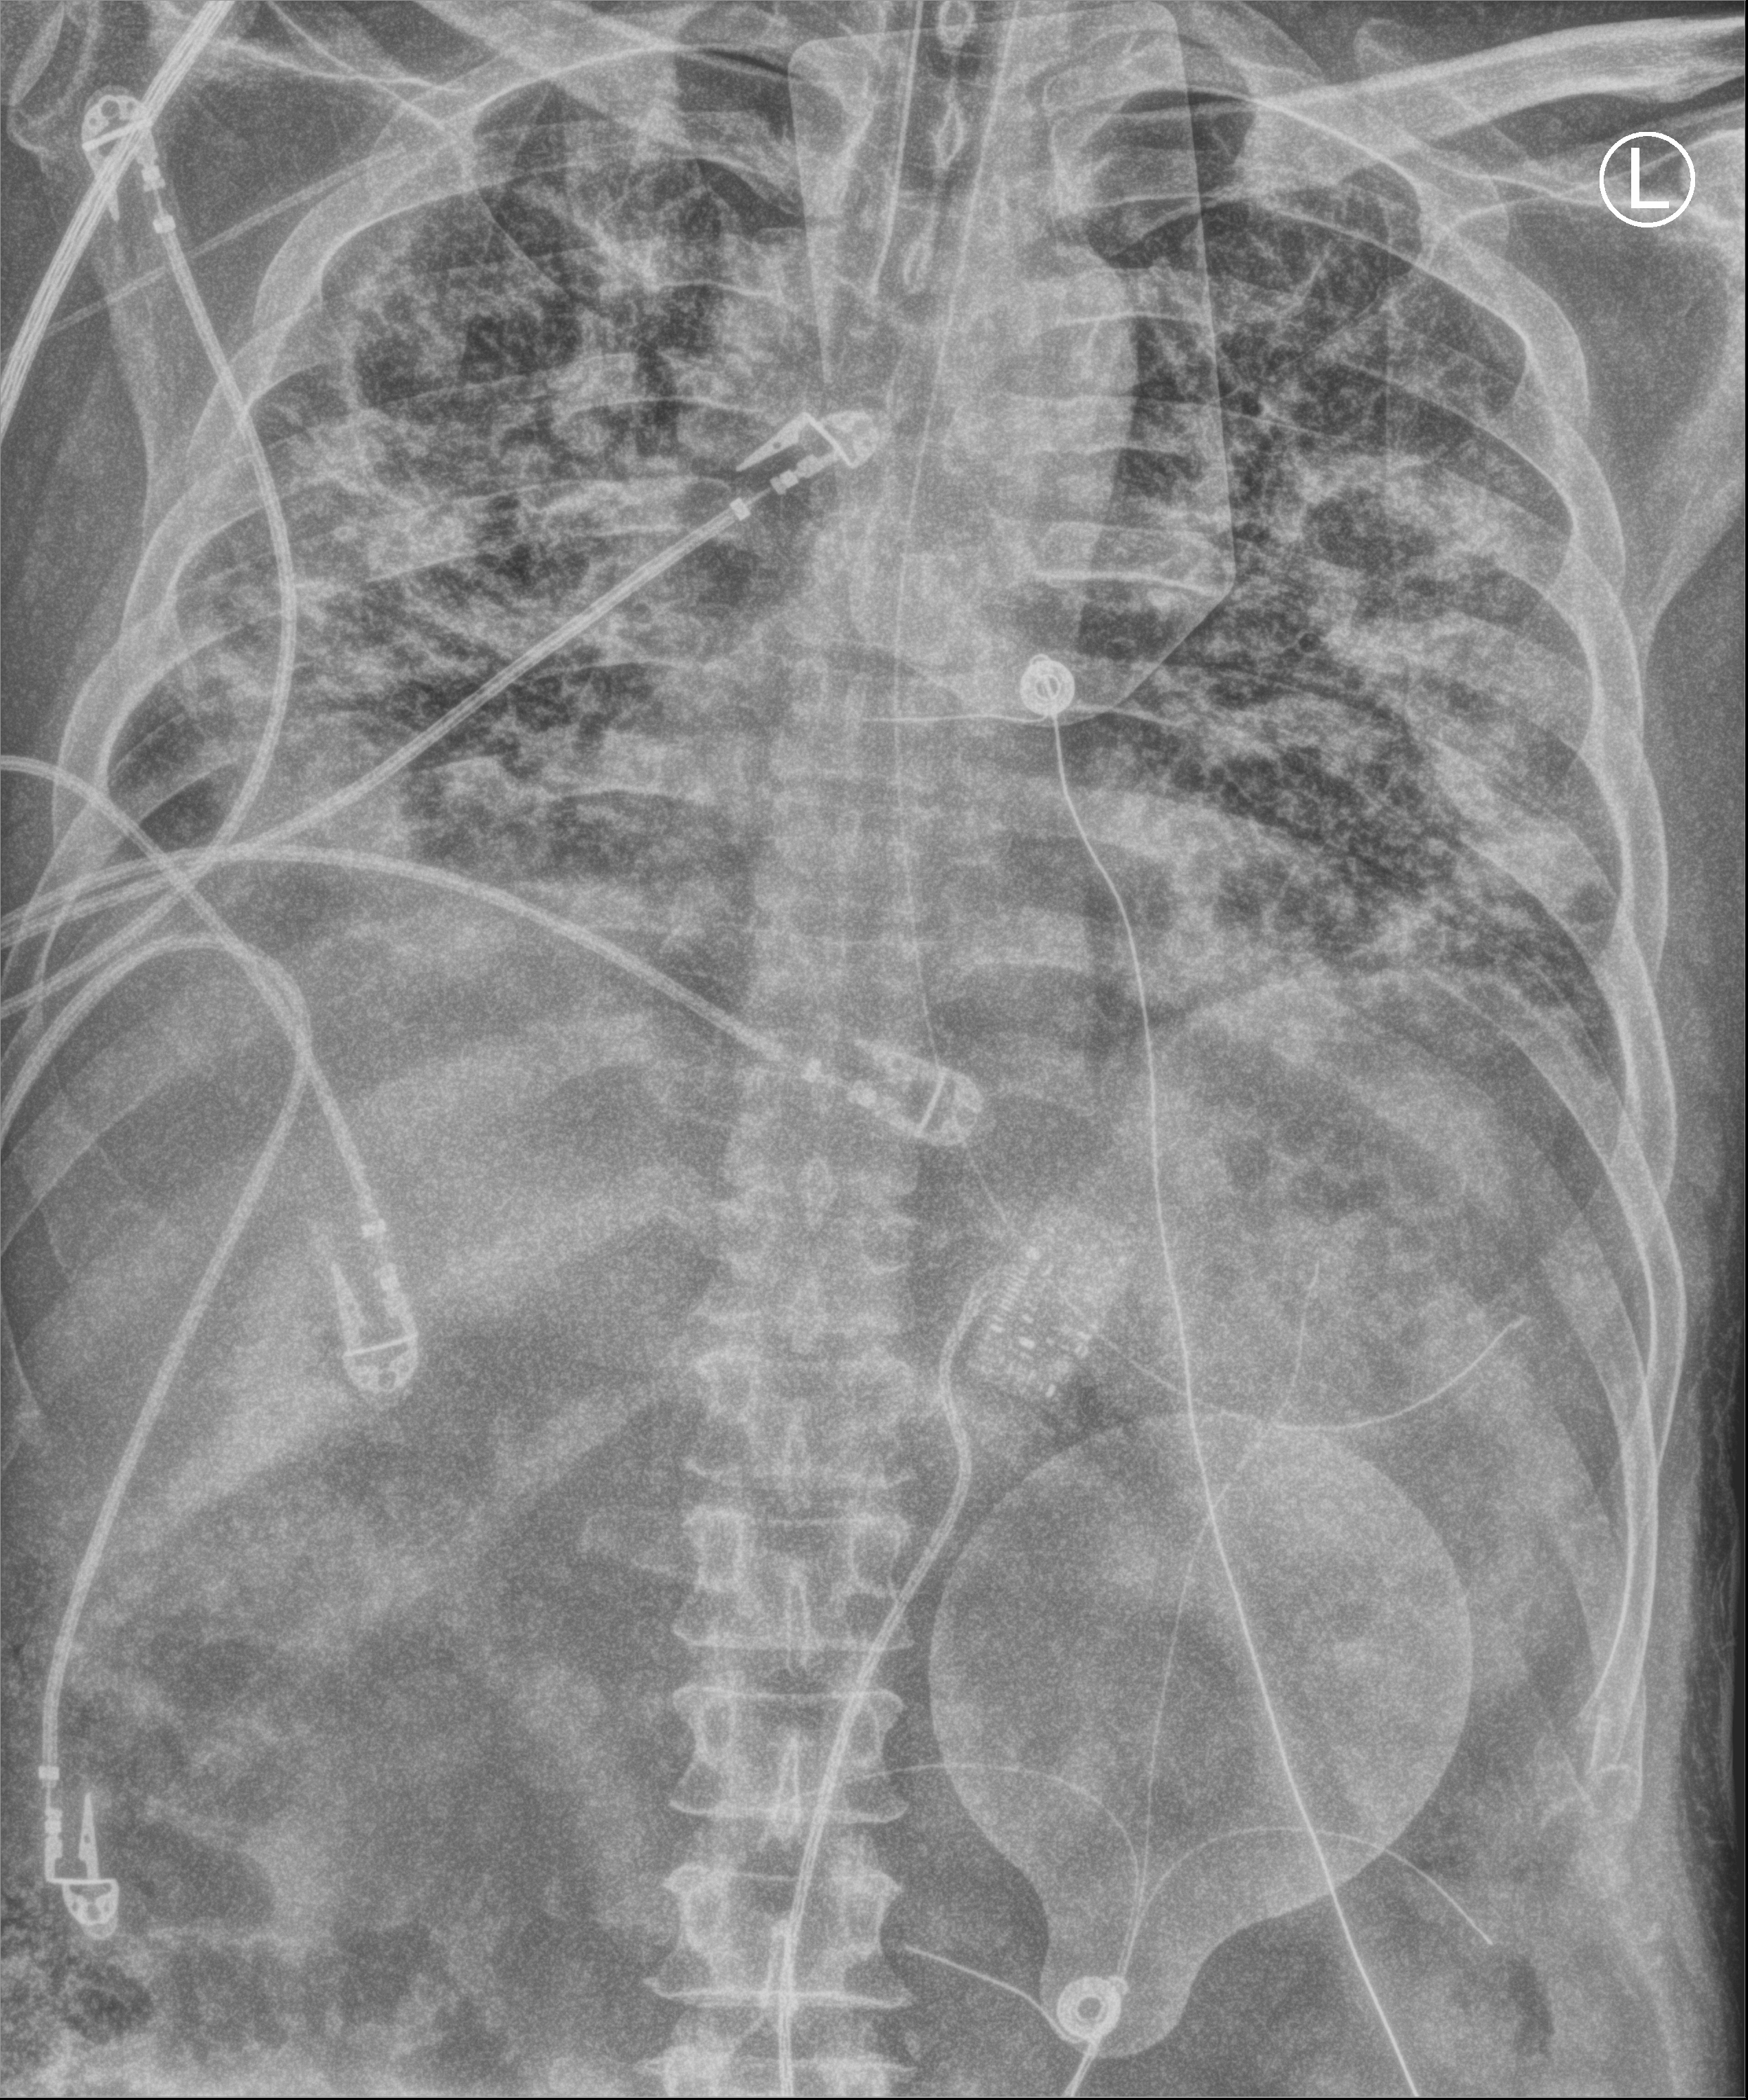
Bedside chest radiograph (computed radiography); anteroposterior (AP) projection. Male patient hospitalised with COVID-19, age 18–59 years.
Hospital-stay facts (about this admission, not read from this image; timing relative to this image not recorded): smoking status (admission record): former.